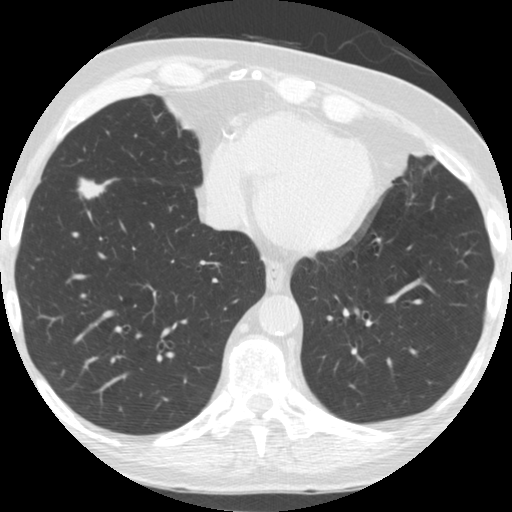
Low-dose screening chest CT, one axial slice; position 68 of 182 along the scan axis; 120 kVp; lung window (W 1500 / L -600 HU); 2.5 mm slice thickness; 512 × 512 image matrix, field of view 320 × 320 mm.
Structures marked on this image (expert manual segmentation):
- lesion 1 (tumor, lower lobe of right lung): bounding box <78,178,115,200> (left, top, right, bottom; pixels)